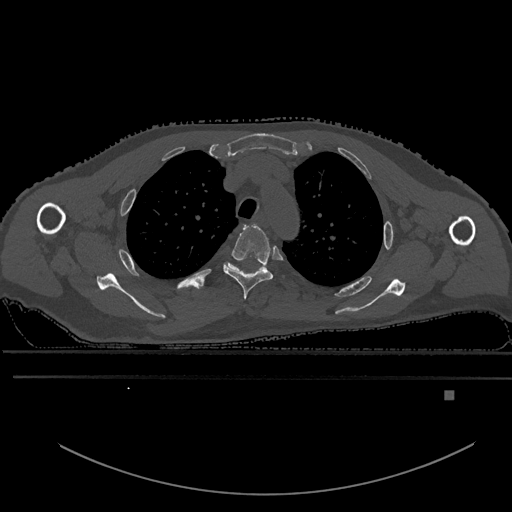
CT including the spine, one axial slice. Slice 446 of 969 in the series (ordered by position). Bone window (W 1800 / L 400 HU). 0.5 mm slice thickness. 512 × 512 image matrix. Male patient, age 82 years. From the clinical record (not read from this slice): primary cancer: prostate; vertebrae with lytic lesions (as recorded): T11, T9, T8, T2.
Annotated regions visible in this slice (semi-automatically segmented with operator editing):
- T3 vertebra: bounding box <223,224,284,300> (left, top, right, bottom; pixels)
- T4 vertebra: <226,262,262,270>